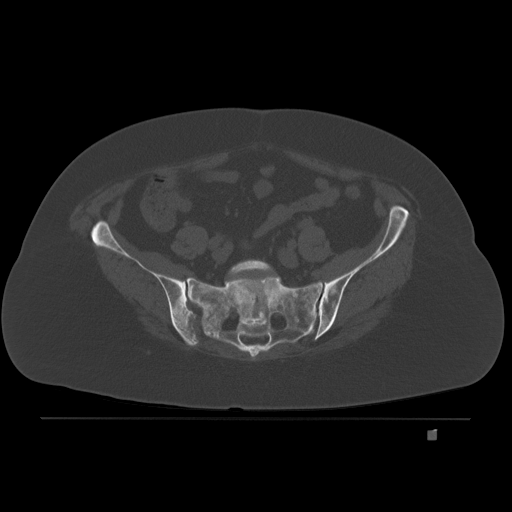
CT including the spine, one axial slice. Position 21 of 221 along the scan axis. Bone window (W 1800 / L 400 HU). 3 mm slice thickness. 512 × 512 image matrix. Patient: female, 63 years. Case-level facts recorded for this patient, not image findings: primary cancer: breast.
Structures marked on this image (semi-automatically segmented with operator editing):
- L5 vertebra: bounding box (x1, y1, x2, y2) in pixels: (227, 259, 274, 277)